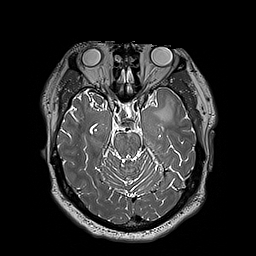
Brain MRI from a brain-tumour surgery series, one axial slice. Slice 125 of 192 in the series (ordered by position). 1 mm slice thickness. 256 × 256 image matrix, field of view 250 × 250 mm. Case-level facts recorded for this patient, not image findings: histopathology: Astrocytoma; WHO grade: 3; IDH mutation: yes; tumour location: Left Insular.
Structures marked on this image (outlined manually by an expert reader):
- tumour: box from (x=154, y=100) to (x=173, y=123) px